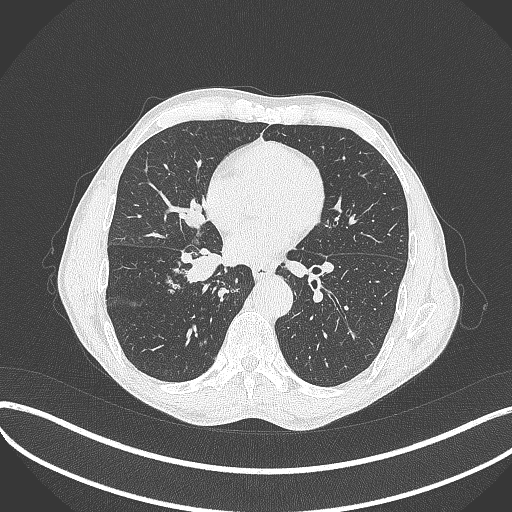
Chest CT, one axial slice. Position 192 of 481 along the scan axis. Lung window (W 1500 / L -600 HU). 1 mm slice thickness. 512 × 512 image matrix. Patient: male, 65 years. From the clinical record (not read from this slice): clinical TNM (as recorded): T2a N0 M0; histopathological grade: G2.
Outlined on this slice (rectangle marked by the reading radiologist):
- lung tumour (recorded histology: squamous cell carcinoma): bounding box <175,246,230,290> (left, top, right, bottom; pixels)